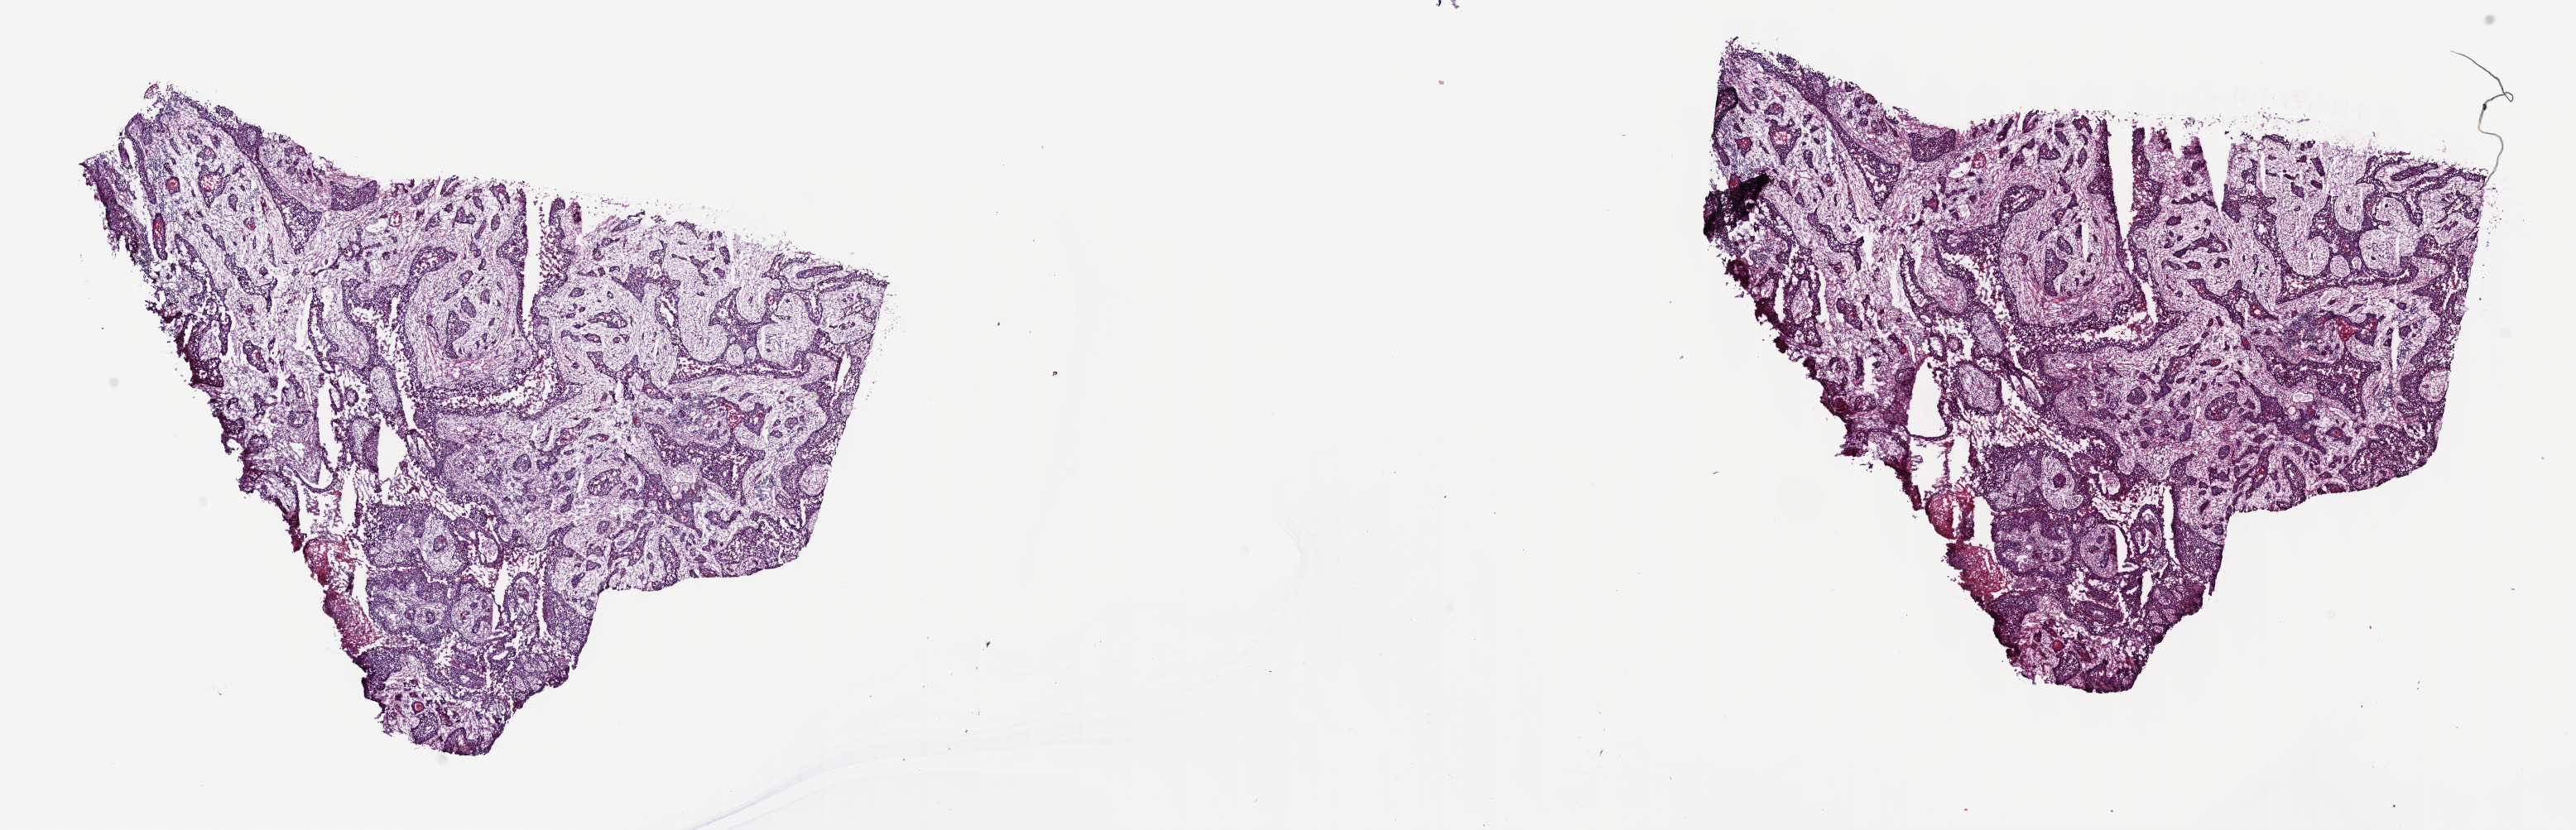
Whole-slide histology image, Hematoxylin and eosin (H&E) stained, a low-resolution overview of the entire scanned area, about 25.2 x 8.1 mm (from a 40x scan), frozen section, sample: primary tumour, esophagus. Female patient; age at initial diagnosis 44 years. Histologic grade: G1 (well differentiated). Slide review estimates, as recorded: tumour cells 96%, tumour nuclei 70%, normal cells 0%, stromal cells 0%, necrosis 4%. Infiltration values recorded for this section: lymphocyte infiltration 5%, monocyte infiltration 0%, neutrophil infiltration 0%.
- TNM: T3 N0 M0
- AJCC pathologic stage: IIA
- pathologic diagnosis: Squamous cell carcinoma, NOS